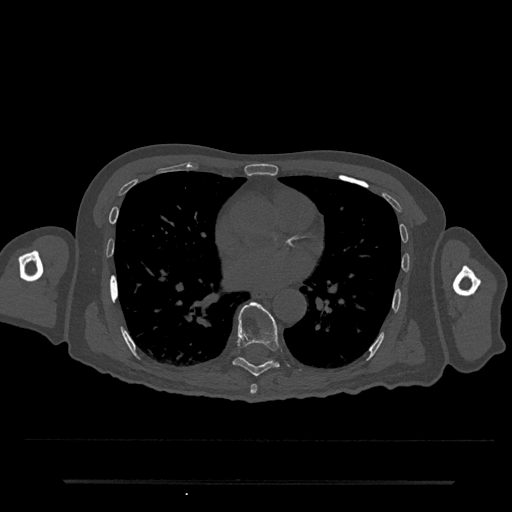
CT including the spine, one axial slice. Slice 417 of 797 in the series (ordered by position). Reconstruction kernel Br40s/3. Bone window (W 1800 / L 400 HU). 0.5 mm slice thickness. 512 × 512 image matrix, field of view 427 × 427 mm. Male patient, age 74 years. Case-level facts recorded for this patient, not image findings: primary cancer: prostate.
Annotated regions visible in this slice (semi-automatic segmentation, software-assisted and operator-edited):
- T7 vertebra: bounding box (x1, y1, x2, y2) in pixels: (250, 384, 258, 394)
- T8 vertebra: (232, 302, 280, 377)